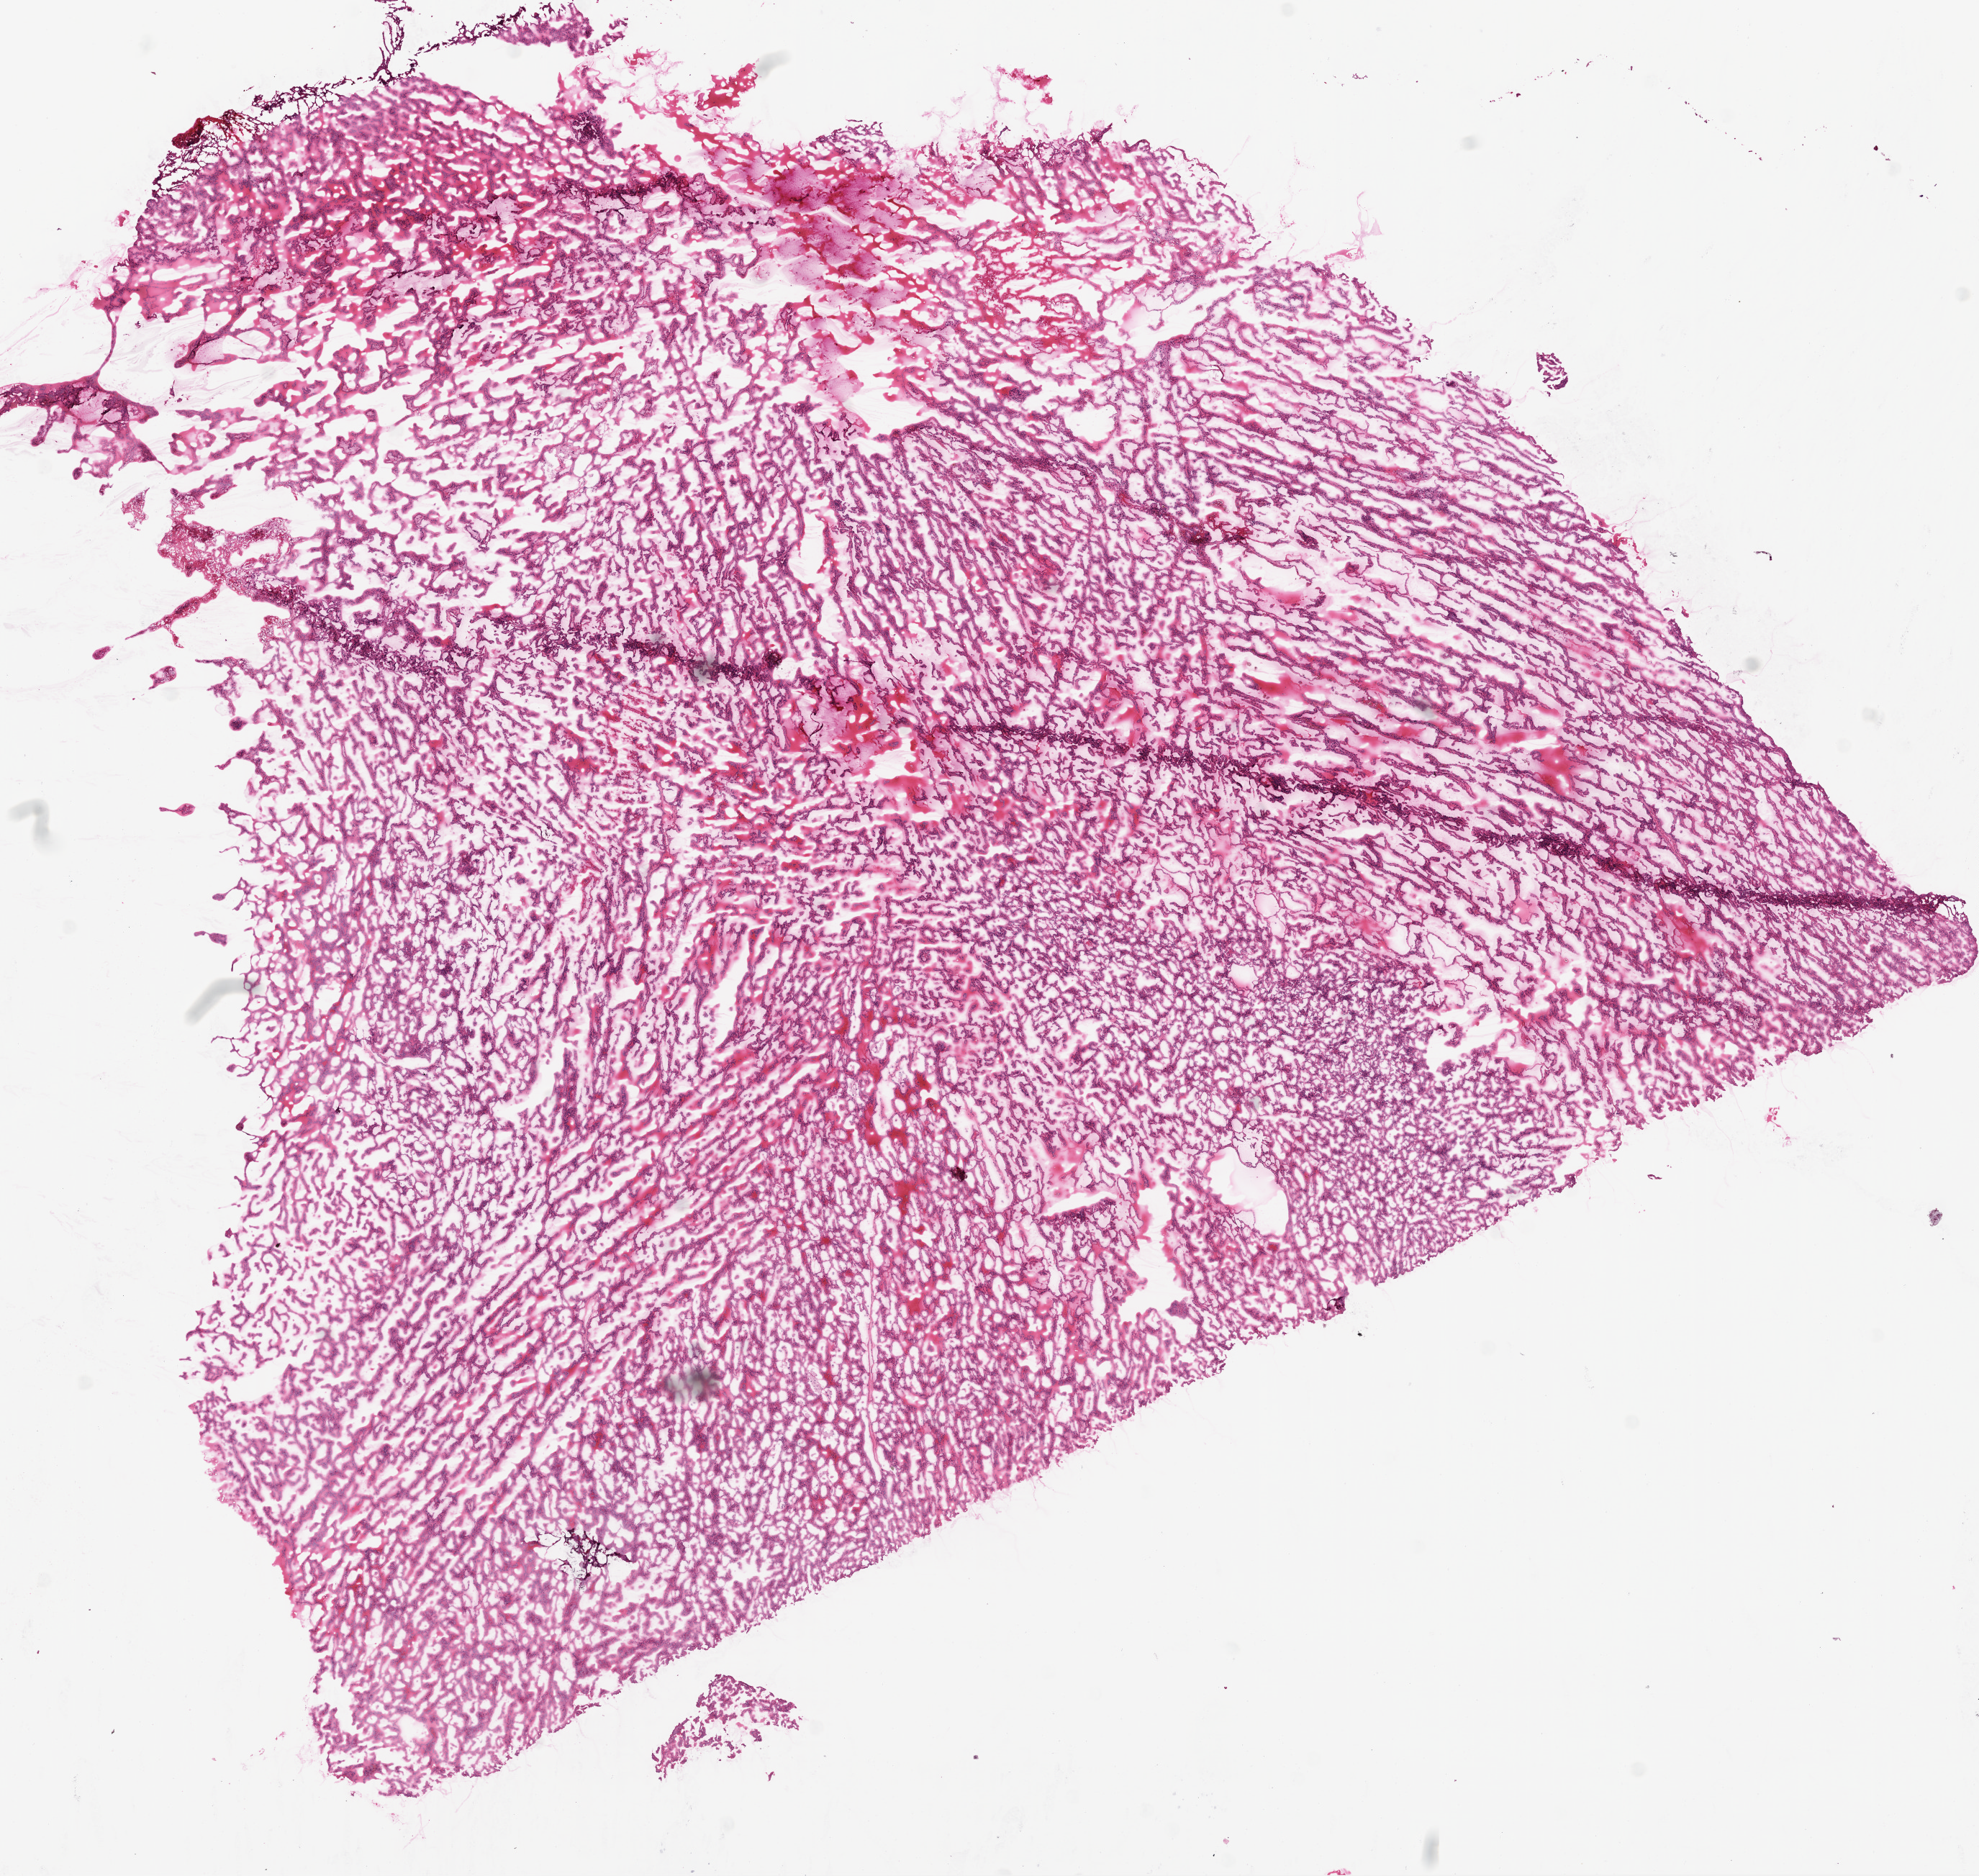
Digitized H&E tissue section (whole slide), a low-resolution overview of the entire scanned area, about 11.0 x 10.5 mm (acquisition: 20x scan); frozen section from the top of the tissue portion; kidney, primary tumour sample. Male, age 74 years at initial diagnosis. Pathologist review of this section (percent, as recorded): tumour cells 92%, tumour nuclei 80%, normal cells 0%, stromal cells 5%, necrosis 3%.
AJCC pathologic stage: II (6th edition). Histologic diagnosis: Papillary adenocarcinoma, NOS.